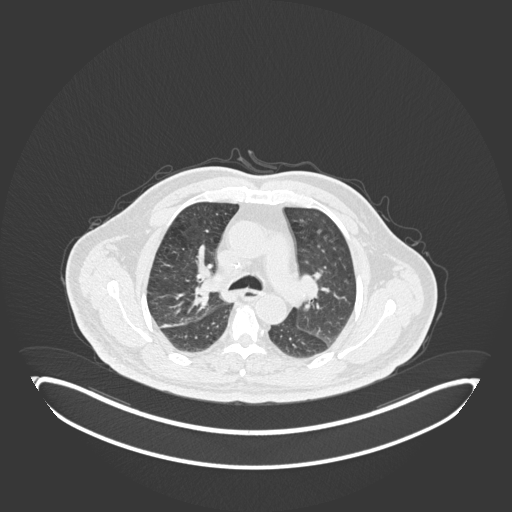
Chest CT, one axial slice; slice 120 of 247 in the series (ordered by position); 120 kVp; lung window (W 1500 / L -600 HU); 1 mm slice thickness; 512 × 512 image matrix, field of view 500 × 500 mm. Patient: male, 72 years. Case-level facts recorded for this patient, not image findings: clinical TNM (as recorded): T1c N0 M0; histopathological grade: G2.
Structures marked on this image (bounding box drawn by a radiologist):
- lung tumour (recorded histology: squamous cell carcinoma): bounding box <194,270,212,307> (left, top, right, bottom; pixels)